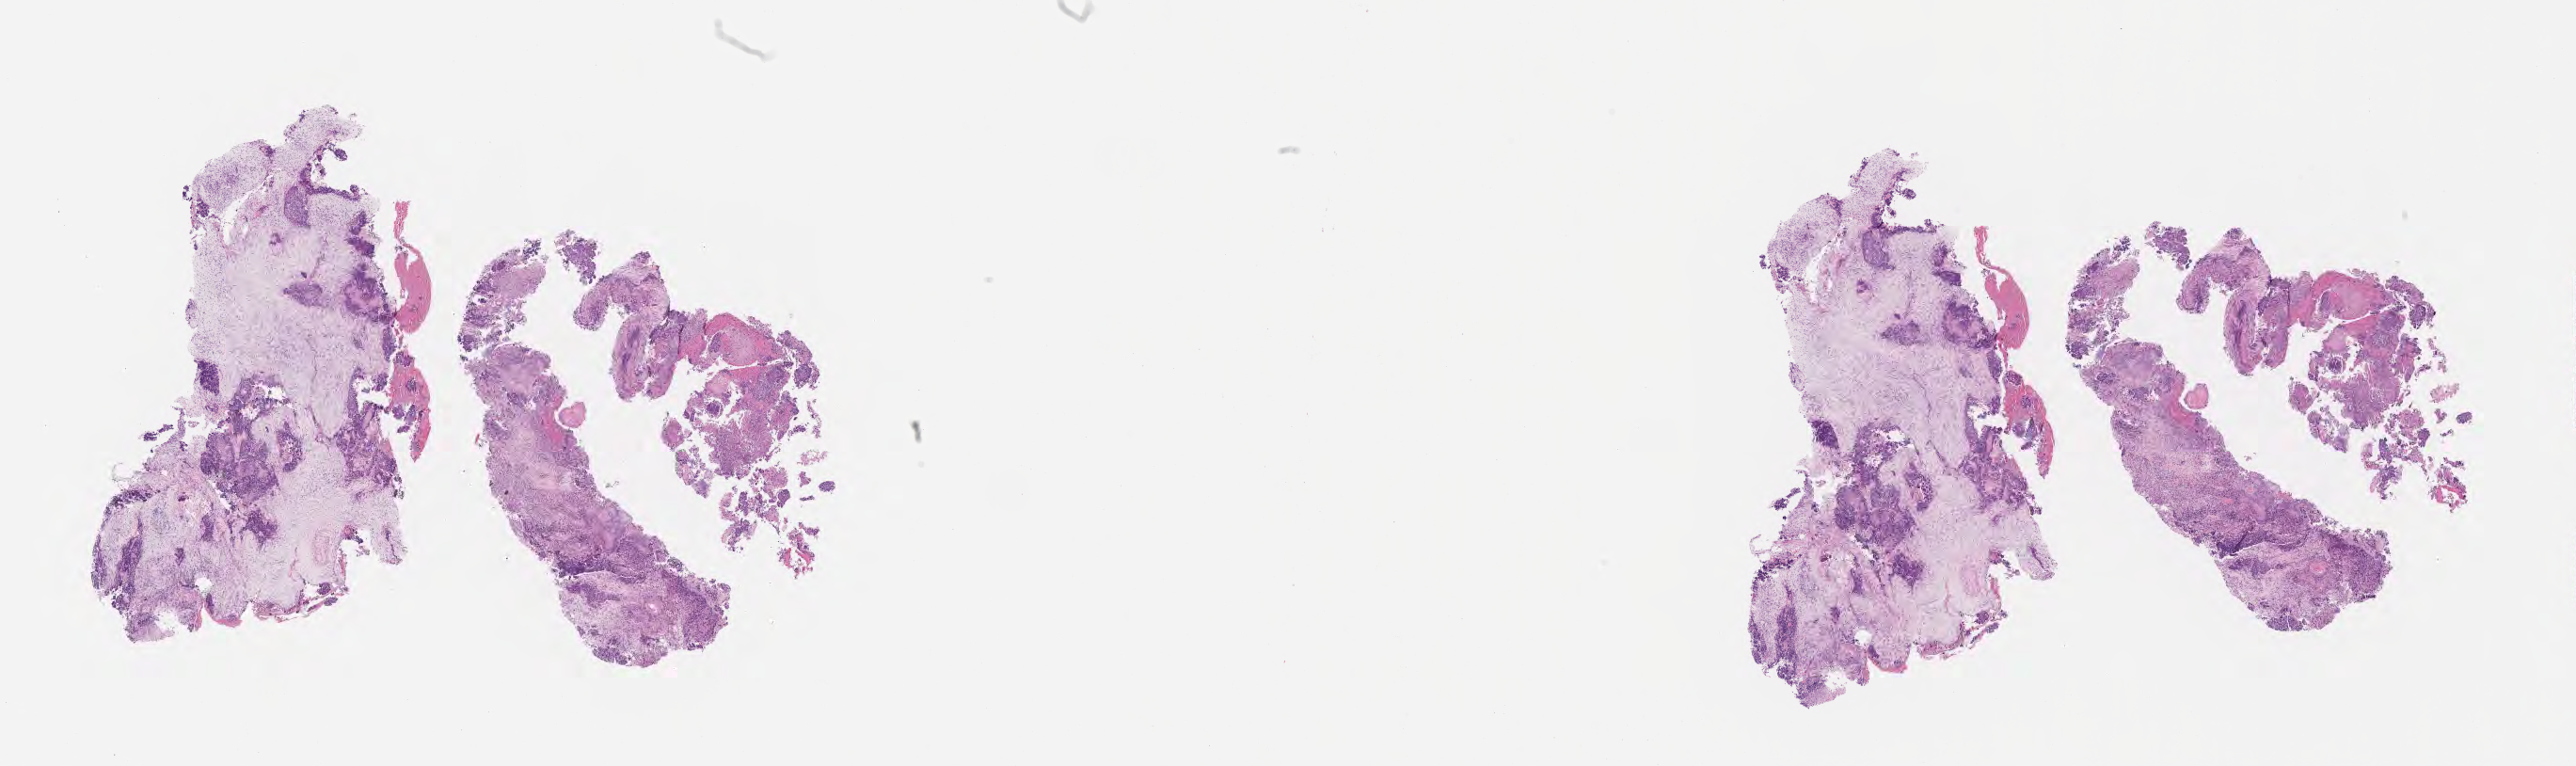
Hematoxylin and eosin (H&E) whole-slide image, low-resolution overview of the scanned area, about 22.1 x 6.6 mm; tumor tissue; anatomic site: cervix. Patient female; aged 47.
- diagnosis: Squamous cell carcinoma, large cell, nonkeratinizing, NOS